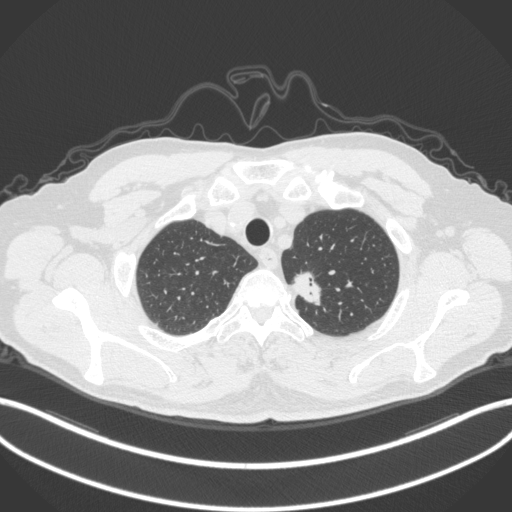
Chest CT, one axial slice. Position 329 of 382 along the scan axis. Reconstruction kernel B31f. Lung window (W 1500 / L -600 HU). 1 mm slice thickness. 512 × 512 image matrix, field of view 400 × 400 mm. Patient: male, 64 years. Case-level facts recorded for this patient, not image findings: clinical TNM (as recorded): T1c N0 M0.
Annotated regions visible in this slice (rectangle marked by the reading radiologist):
- lung tumour (recorded histology: adenocarcinoma): box from (x=290, y=266) to (x=324, y=309) px